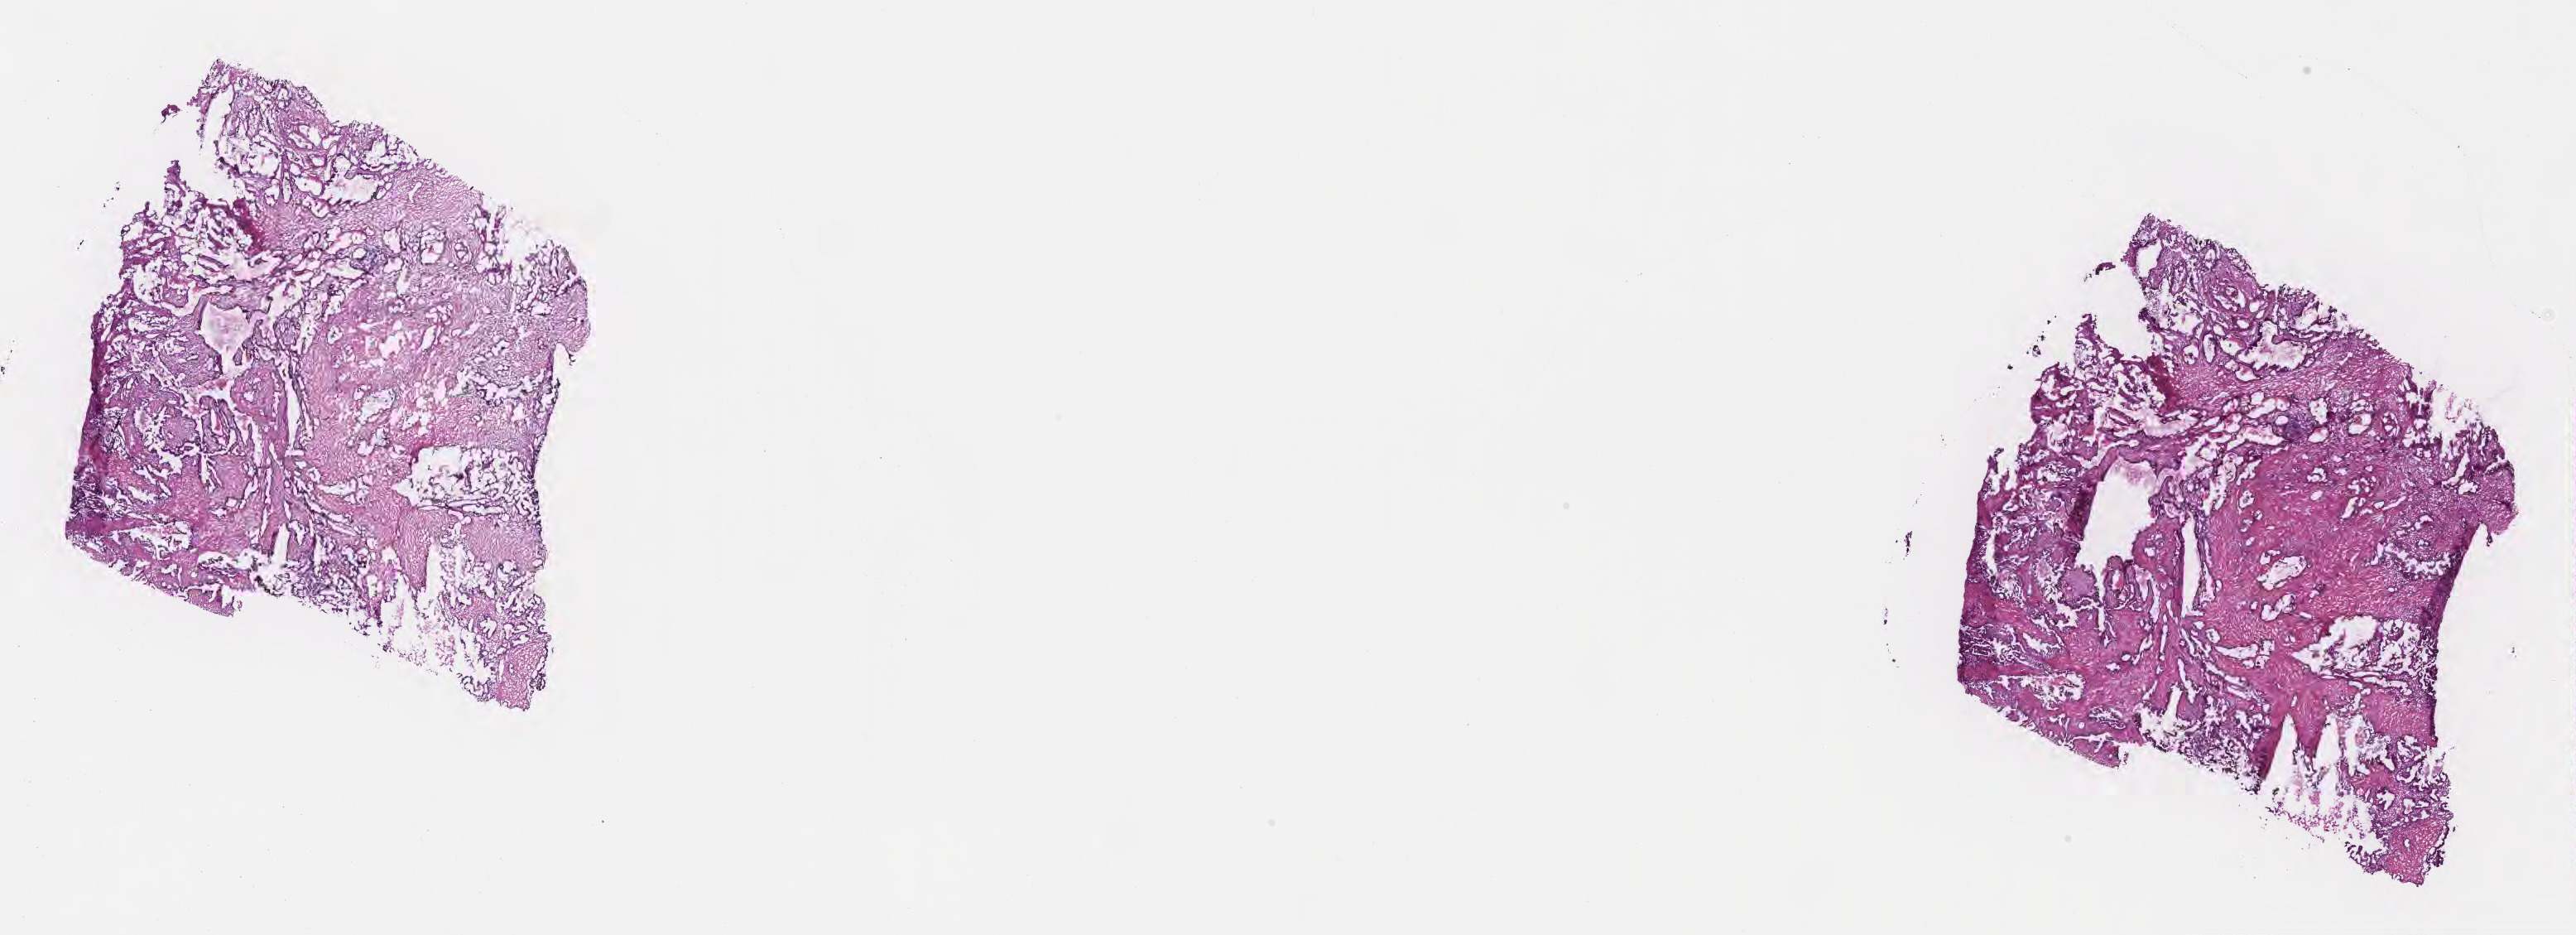
Digitized H&E-stained section — low-resolution overview of the scanned area, about 25.2 x 9.1 mm, frozen section (tissue freezing medium), specimen: primary tumor, anatomic site: head of pancreas. Male patient; age at initial diagnosis 71 years. Tumor grade: G2 (moderately differentiated). Composition of this section per pathologist review: tumor cells 51%, tumor nuclei 90%, stromal cells 46%, necrosis 3%, normal cells 0%. Infiltration values recorded for this section: lymphocyte infiltration 6%, monocyte infiltration 1%, neutrophil infiltration 0%.
Histologic diagnosis: Infiltrating duct carcinoma, NOS. AJCC pathologic stage: Stage III.